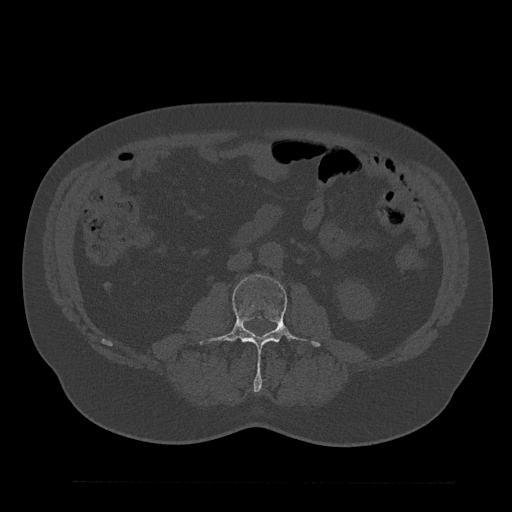
CT including the spine, one axial slice. Reconstruction kernel Br40s/3. 120 kVp. Bone window (W 1800 / L 400 HU). 512 × 512 image matrix, field of view 430 × 430 mm. Male patient, age 61 years. From the clinical record (not read from this slice): primary cancer: prostate.
Annotated regions visible in this slice (semi-automatic segmentation, software-assisted and operator-edited):
- L3 vertebra: bounding box <198,274,321,391> (left, top, right, bottom; pixels)